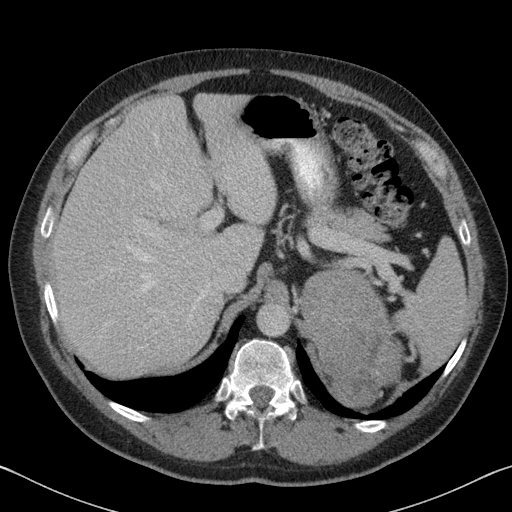
Contrast-enhanced abdominal CT, one axial slice; slice 60 of 88 in the series (ordered by position); reconstruction kernel B31f; 120 kVp; soft-tissue window (W 400 / L 40 HU); 3 mm slice thickness; 512 × 512 image matrix. Male patient, age 51 years. From the clinical record (not read from this slice): diagnosis: adrenocortical carcinoma; tumour side: left adrenal; tumour size at pathology: 16.5 cm; Ki-67 index: 30 %; stage (as recorded): 2.
Annotated regions visible in this slice (semi-automatically segmented with operator editing):
- mass: box from (x=301, y=271) to (x=400, y=405) px